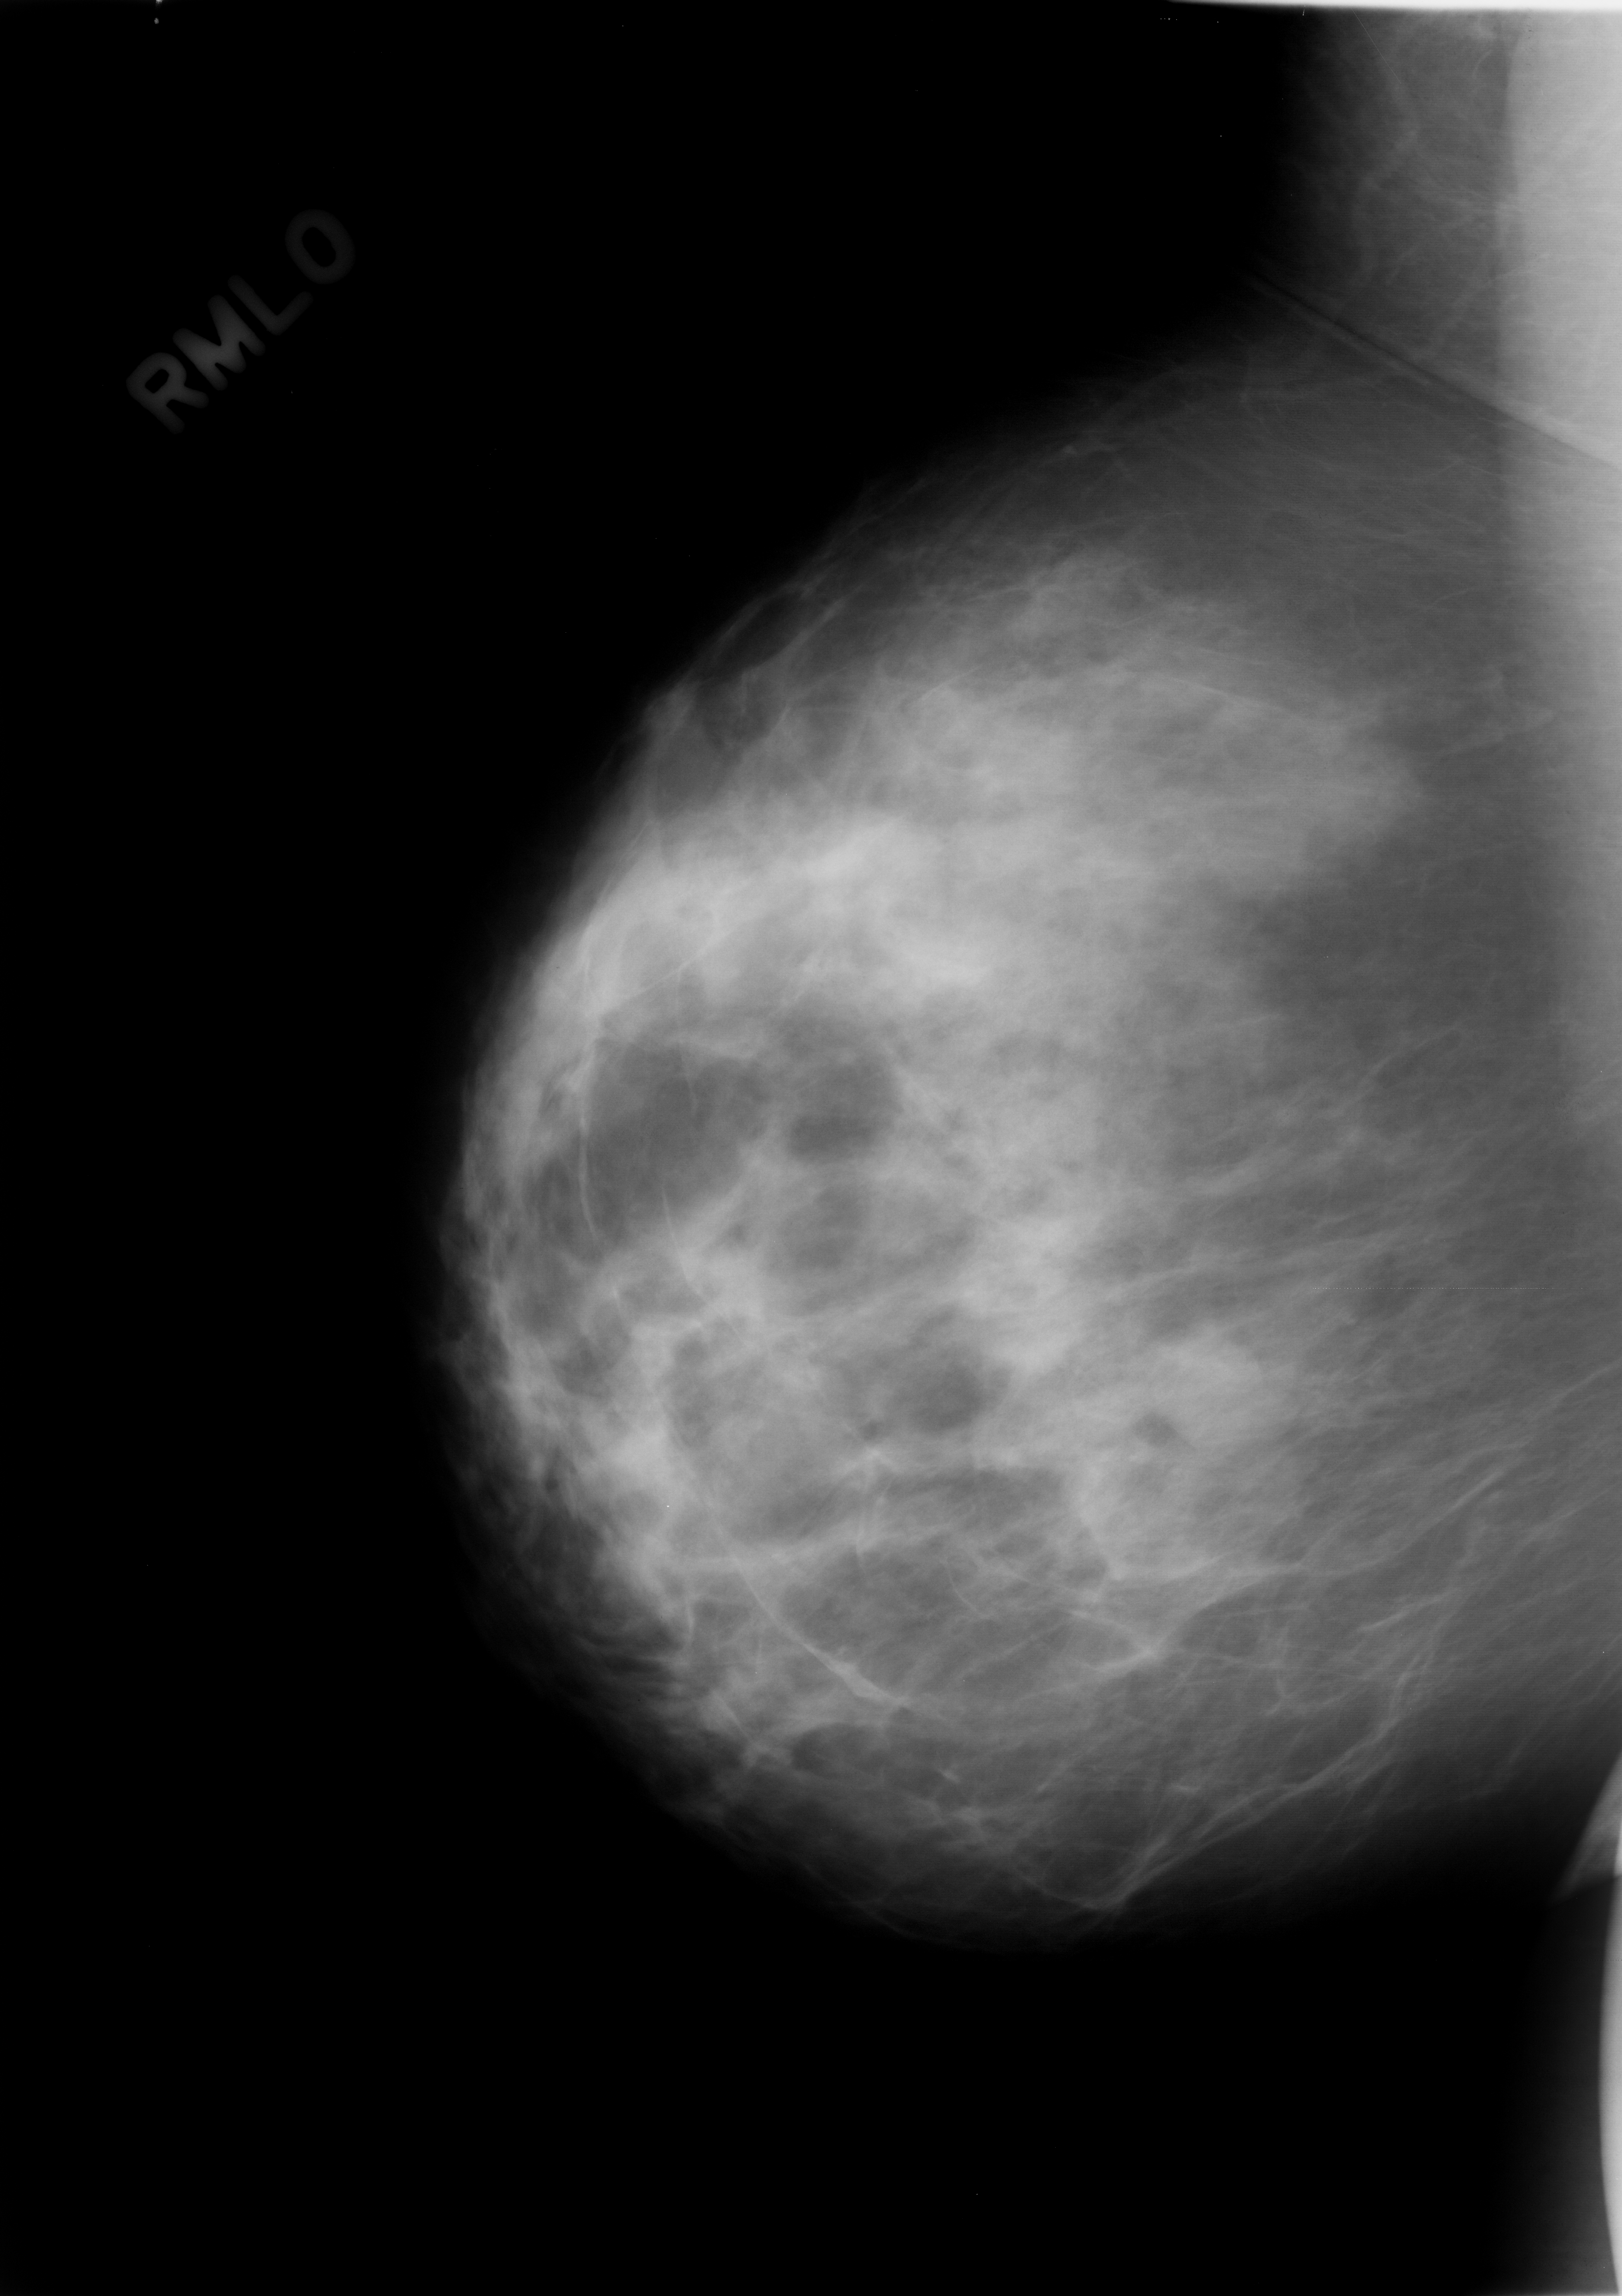
Scanned film-screen mammogram; right breast; MLO view.
- Radiologist-marked abnormalities on this image: mass, shape lobulated, margins circumscribed; BI-RADS assessment category 3; subtlety rating 4 on a 1 (subtle) to 5 (obvious) scale; pathology (as recorded): benign.